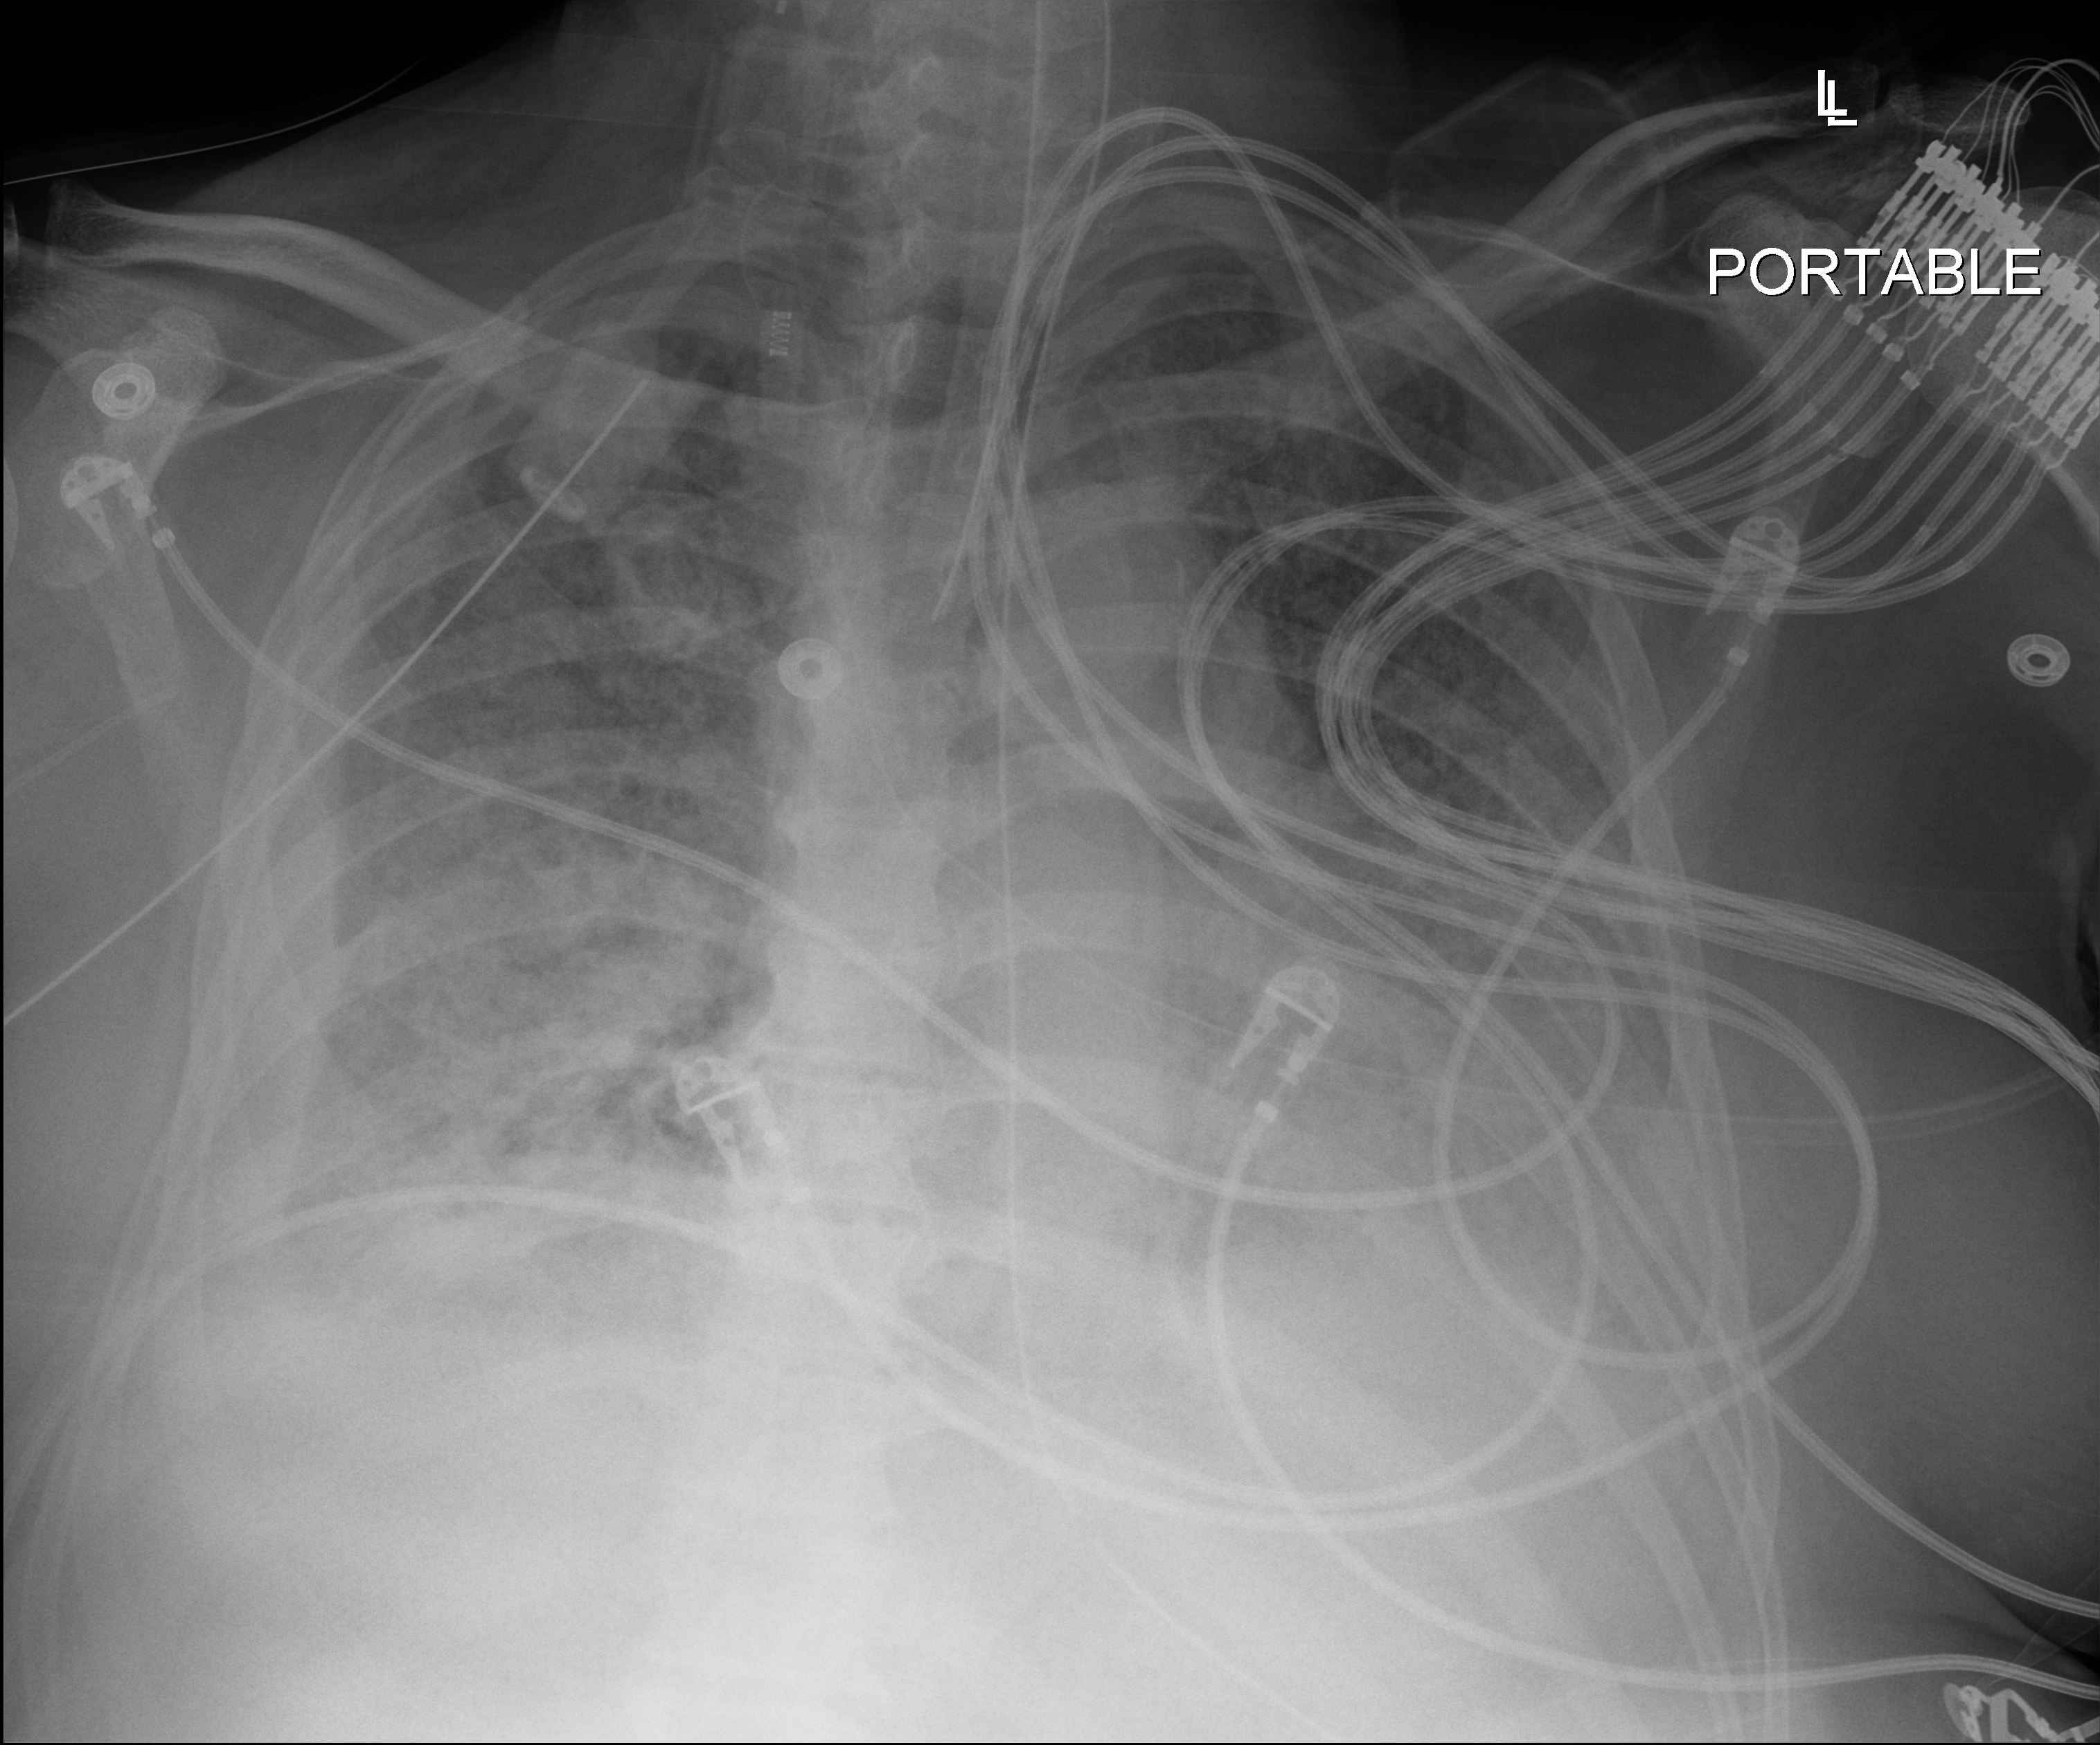
Portable chest radiograph; anteroposterior (AP) projection. Patient hospitalised with COVID-19; male, aged 60–74 years.
From the hospital-stay record, not from the radiograph (when in the stay this image was taken is not recorded): other chronic lung disease (admission record): no; mechanically ventilated during this hospital stay: yes.